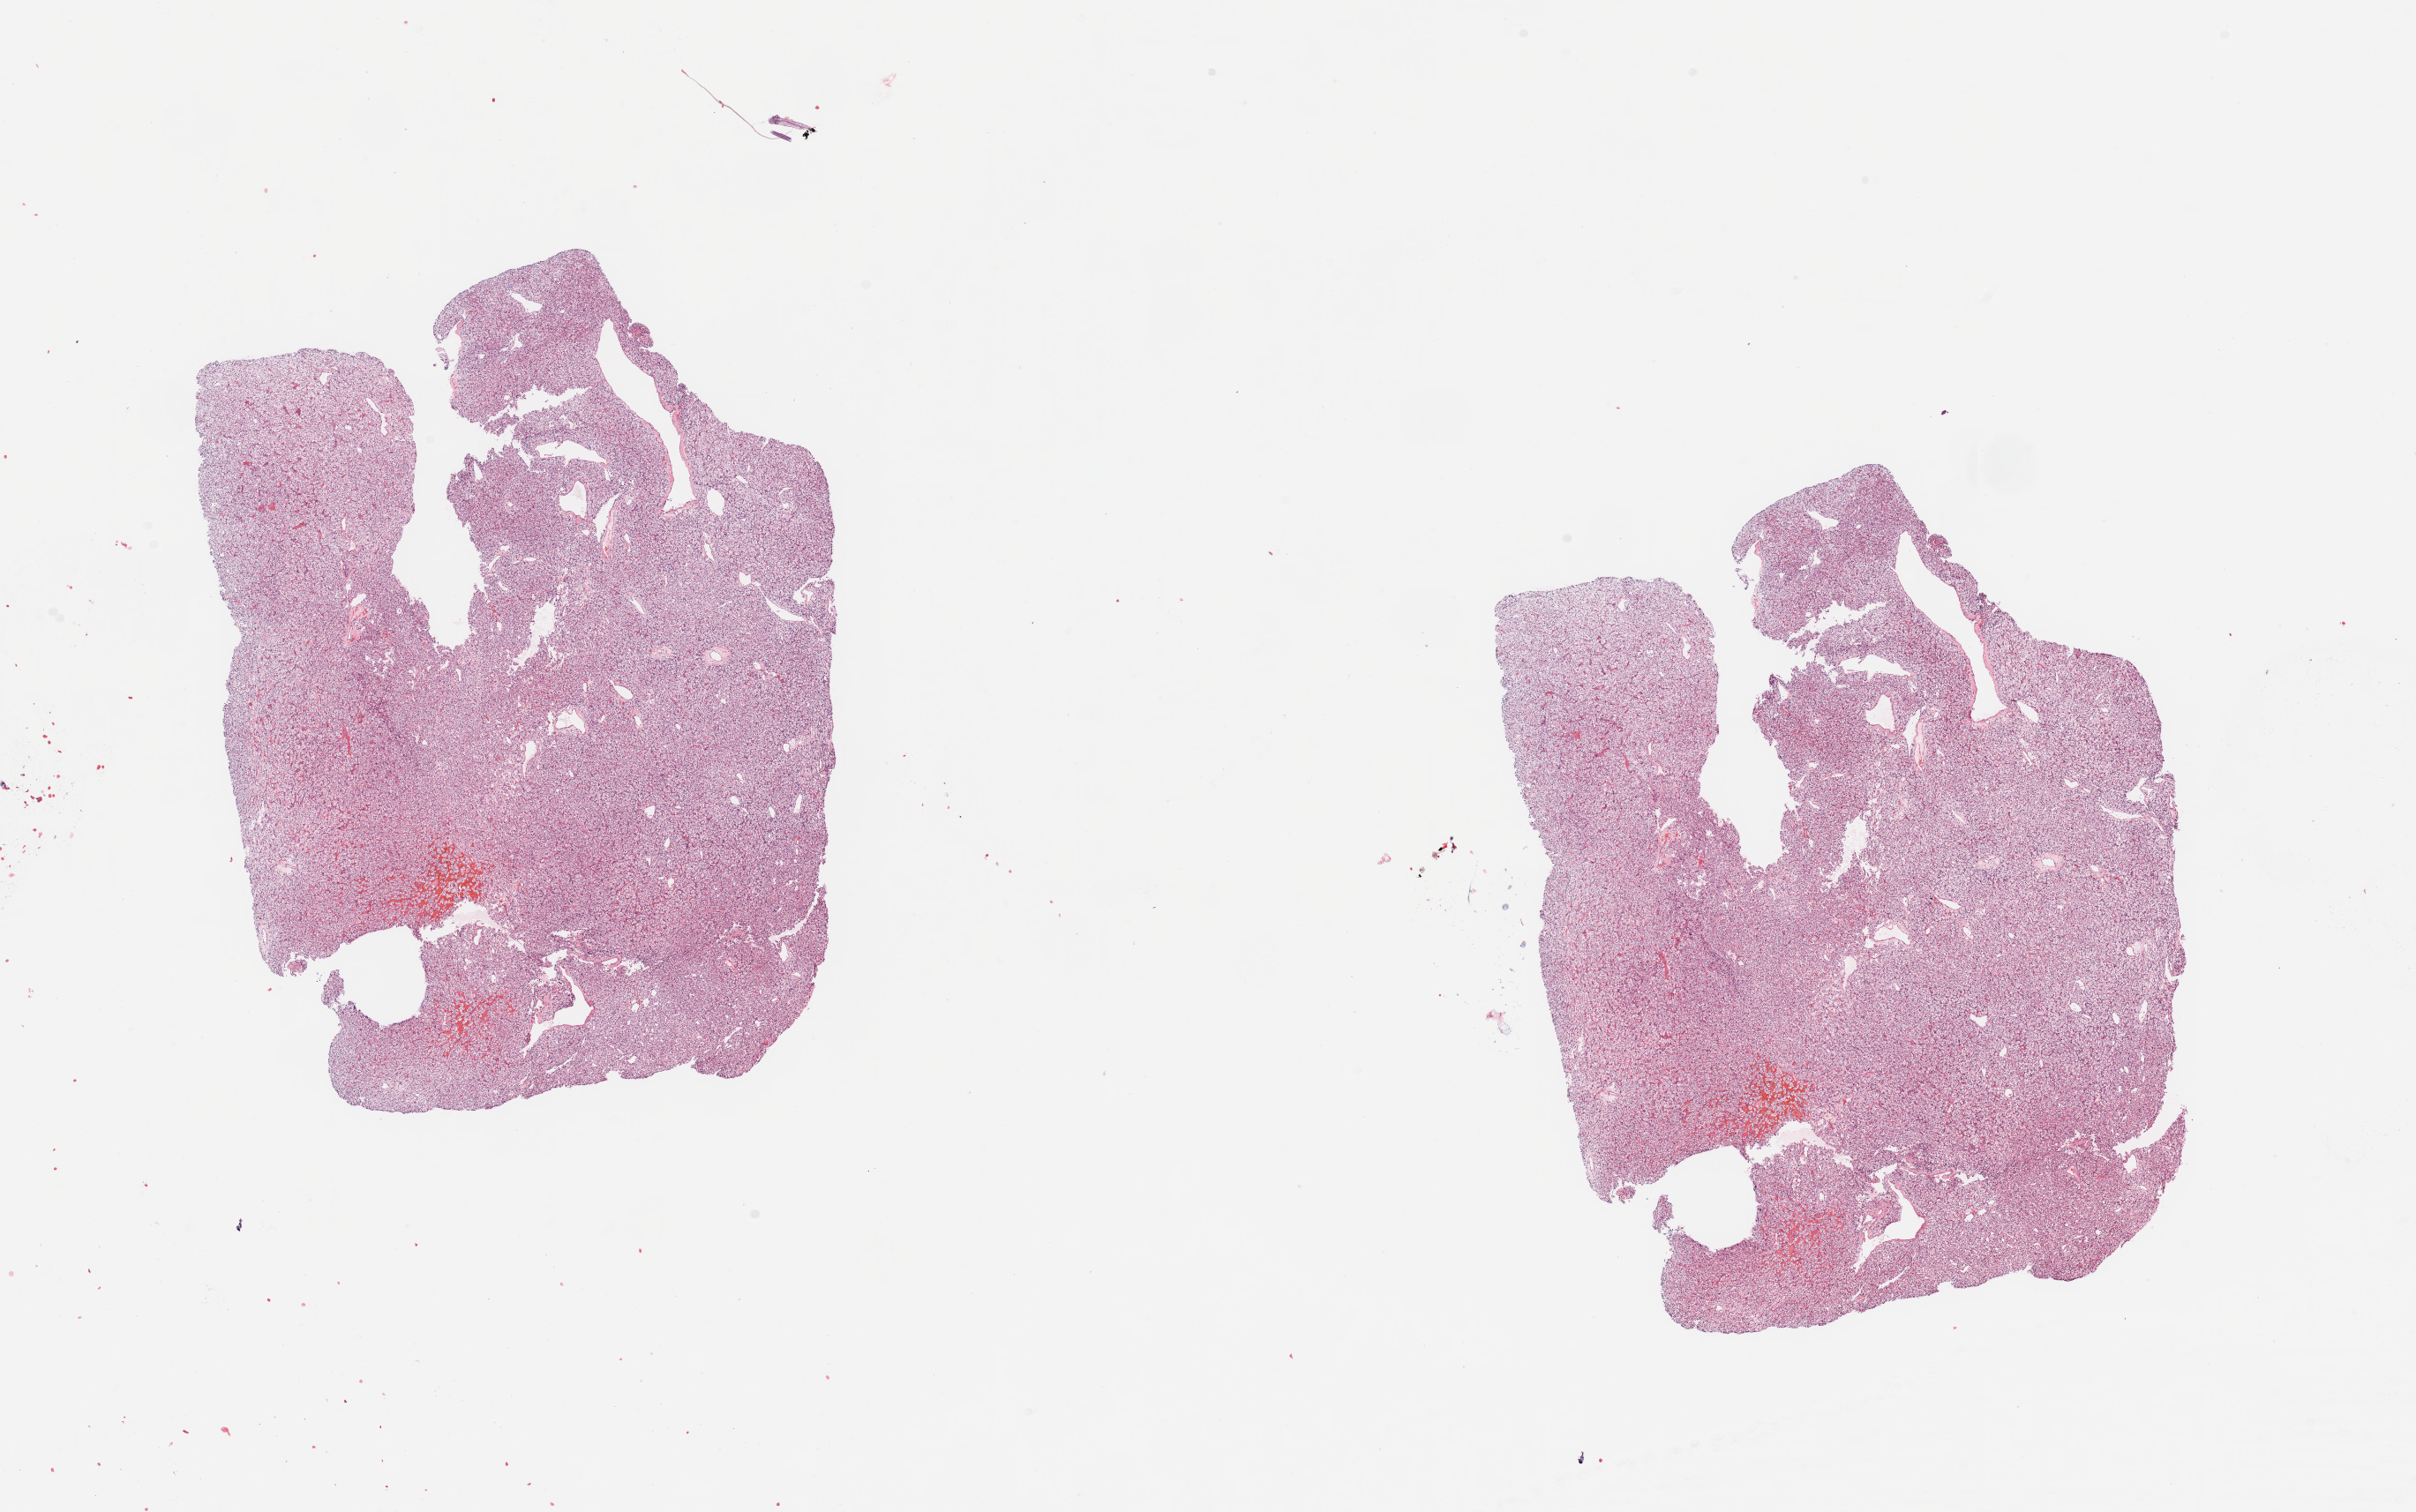
Whole-slide histology image, Hematoxylin and eosin (H&E) stained — whole scanned area (about 21.7 x 13.6 mm, acquisition: 20x scan) shown as a low-resolution overview, tumour tissue sample, kidney. Female, 70 y/o. Histologic grade: G2 (moderately differentiated).
AJCC pathologic stage: II. Diagnosis: Renal cell carcinoma, NOS.